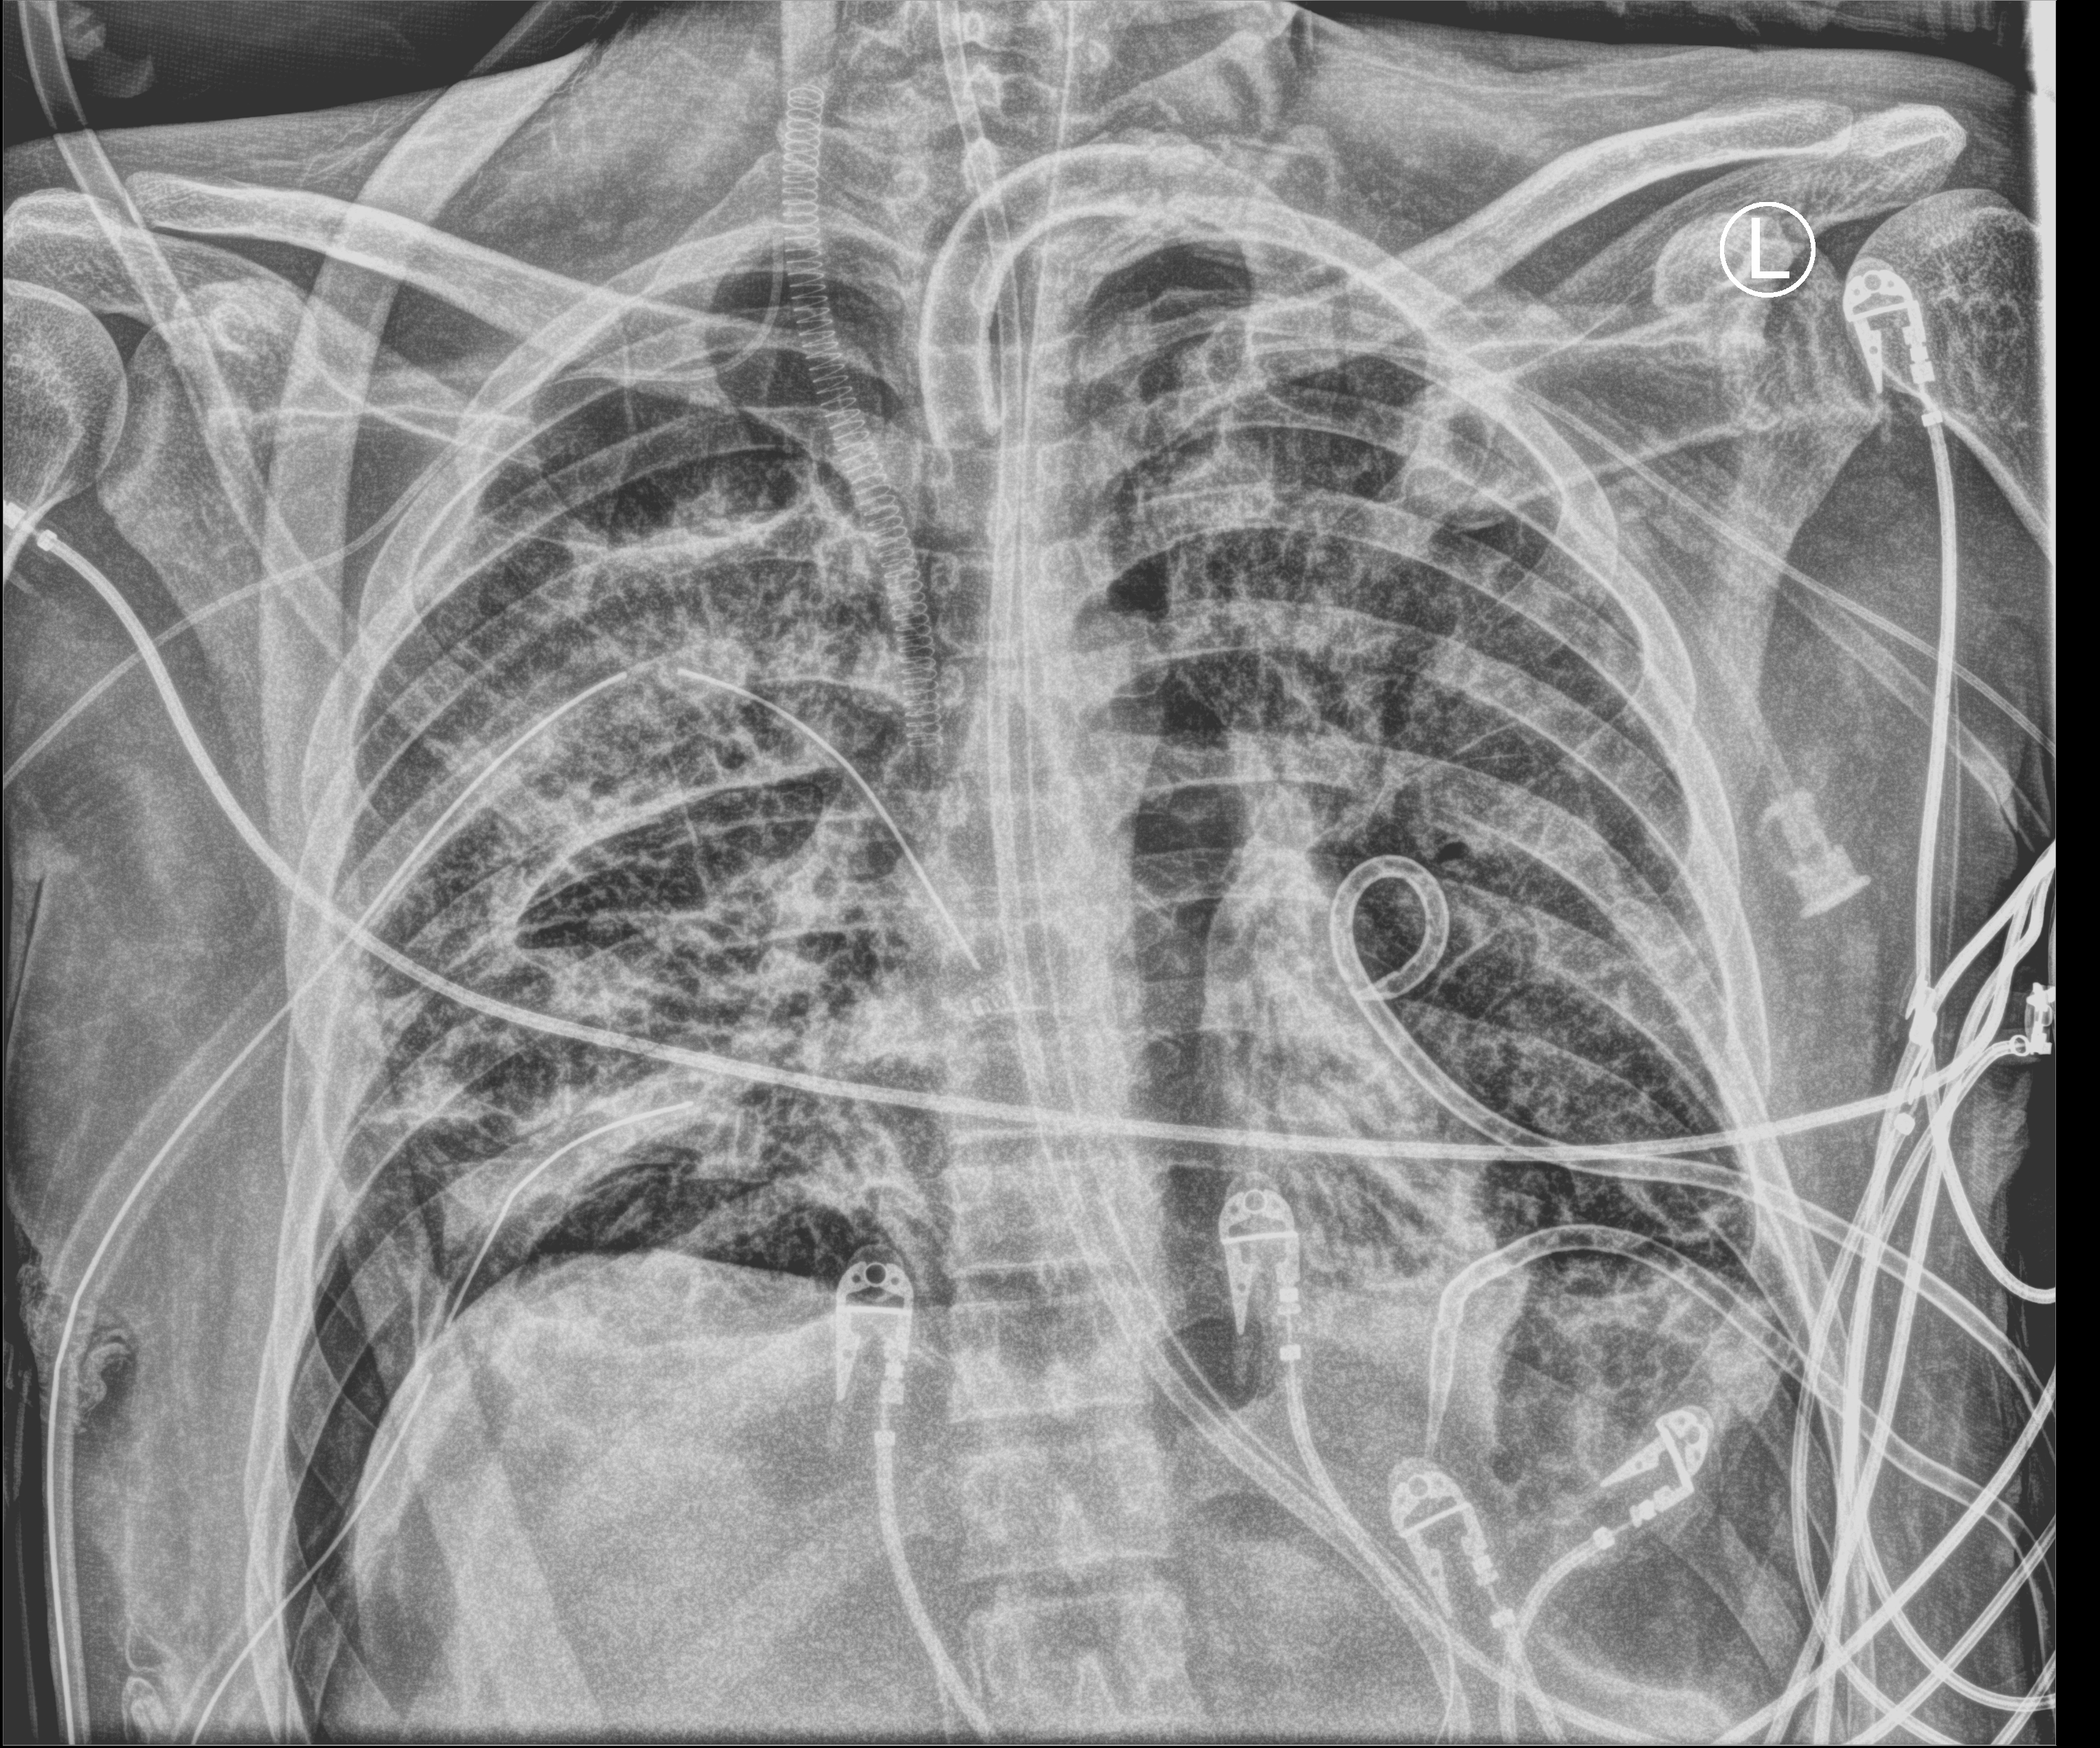
Chest X-ray (portable); anteroposterior (AP) projection. Patient hospitalised with COVID-19, aged 18–59 years.
Admission-level facts for this patient (not findings on this image; timing relative to this image not recorded): other chronic lung disease (admission record): no; diabetes (admission record): no; admitted to intensive care during this hospital stay: yes.